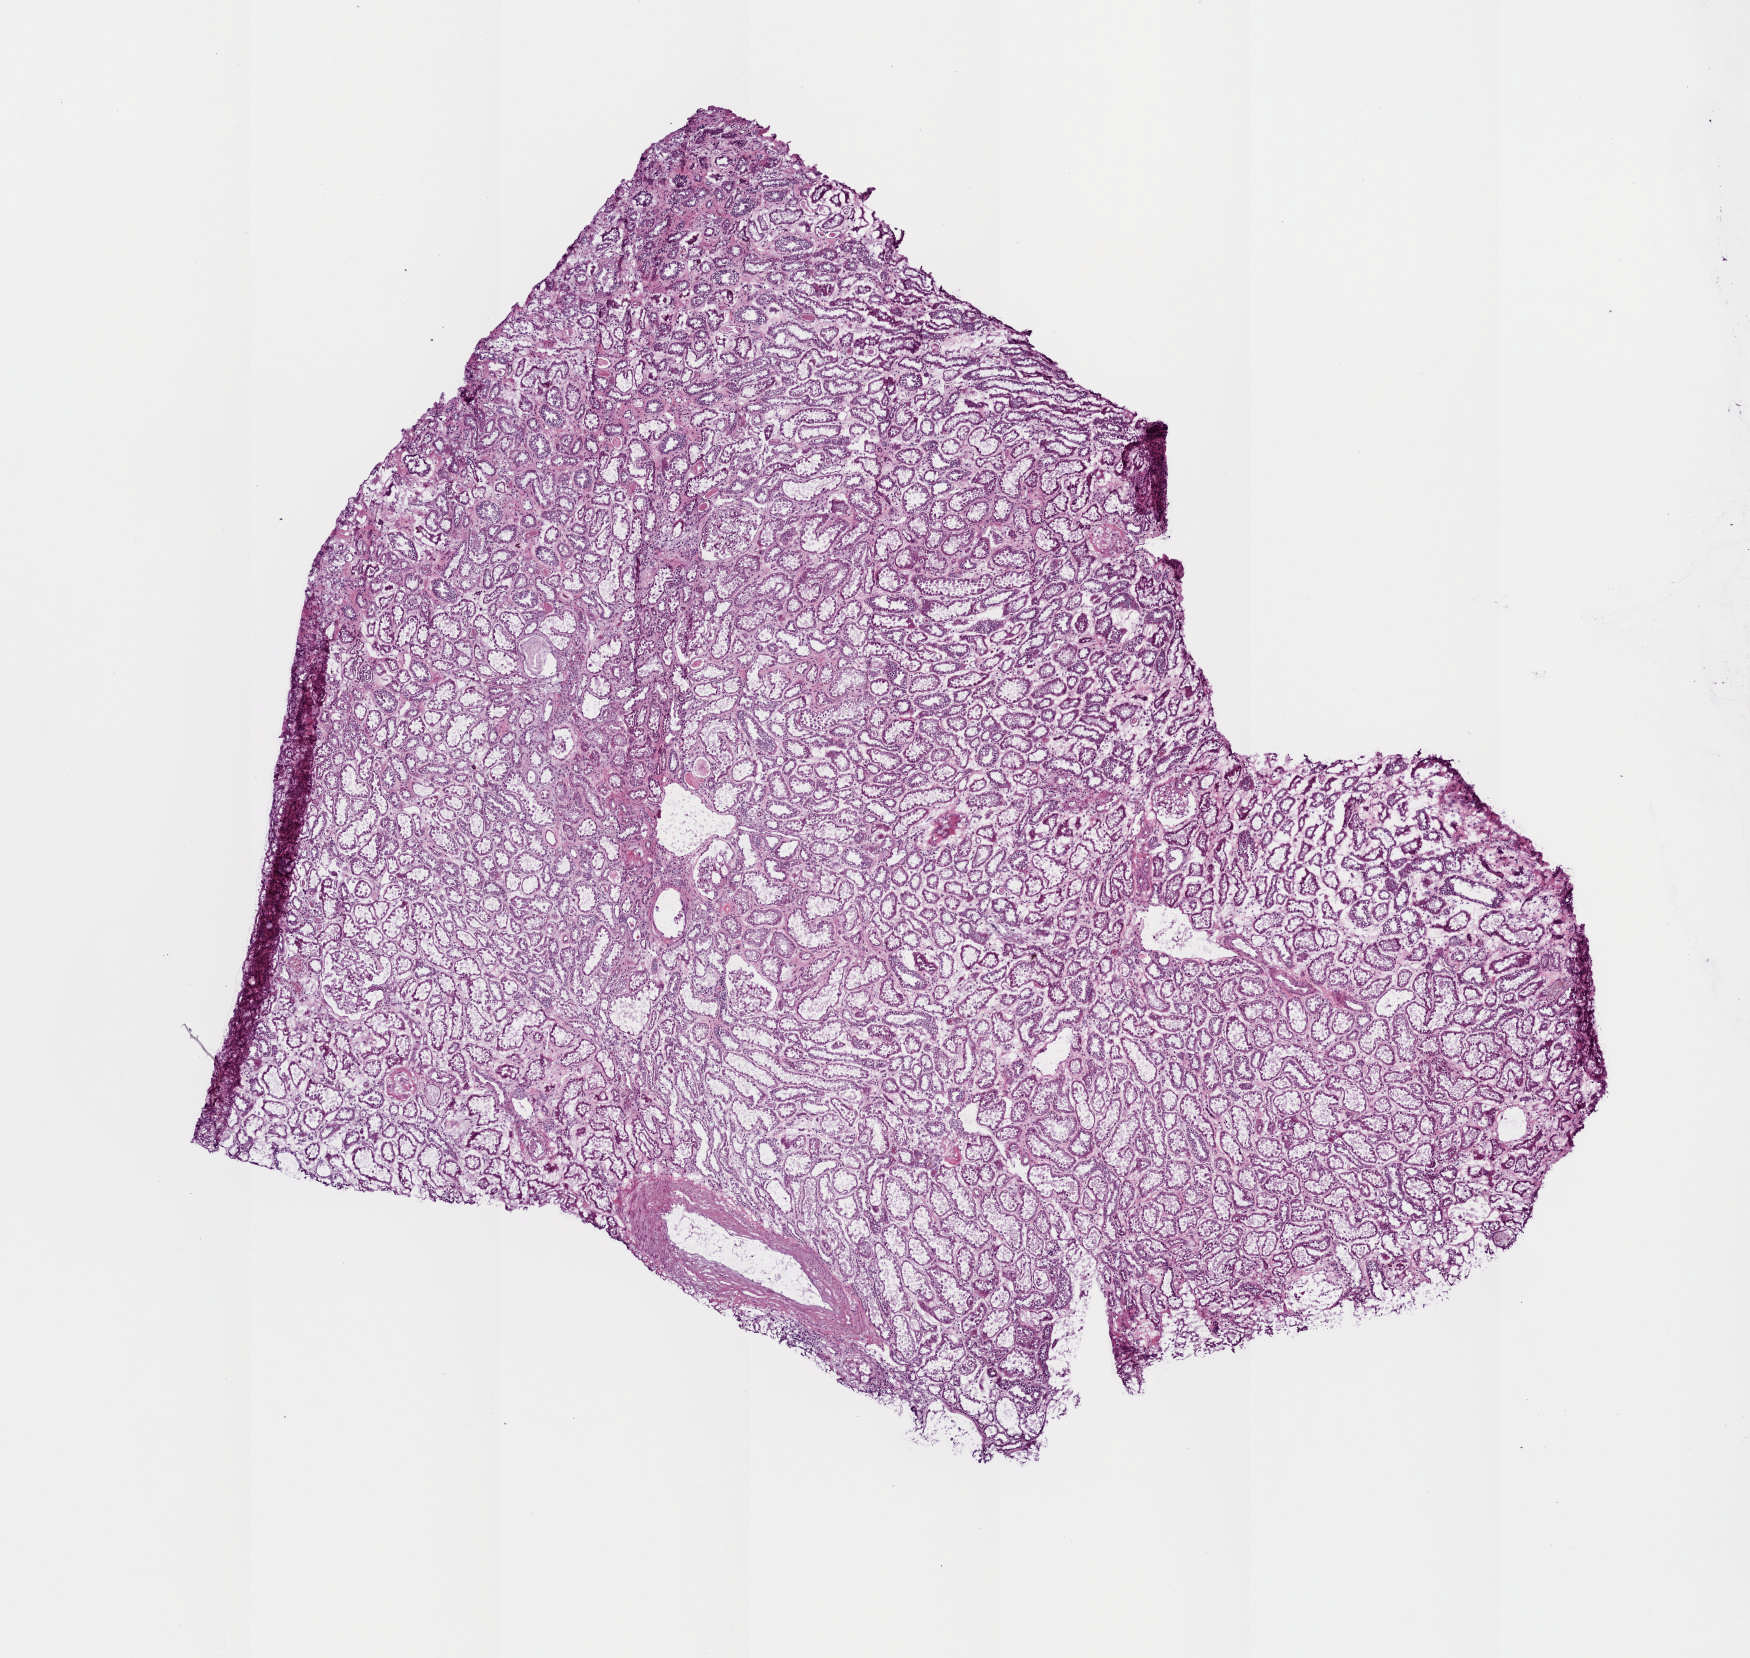
Digitized H&E tissue section (whole slide), a low-resolution overview of the entire scanned area, about 7.0 x 6.7 mm (acquisition: 20x scan); frozen section from the top of the tissue portion; kidney, solid tissue normal (non-tumour tissue) sample. Patient: male, age at initial diagnosis 53 years.
This section: solid tissue normal (non-tumour) sample from the same patient. Patient diagnosis: Papillary adenocarcinoma, NOS.